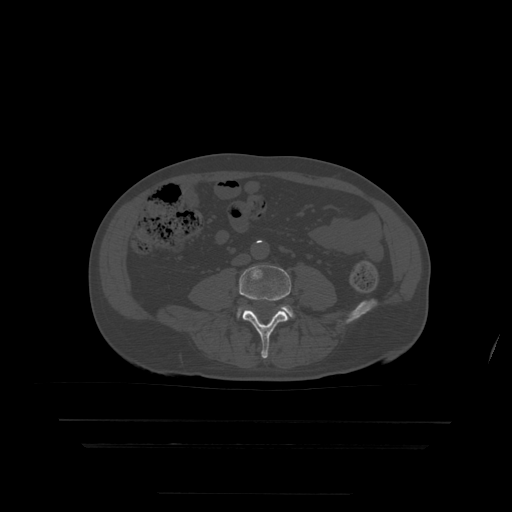
CT including the spine, one axial slice; position 91 of 522 along the scan axis; bone window (W 1800 / L 400 HU); 512 × 512 image matrix. Patient age 68 years. Case-level facts recorded for this patient, not image findings: primary cancer: urothelial.
Outlined on this slice (semi-automatic segmentation, software-assisted and operator-edited):
- L4 vertebra: bounding box (x1, y1, x2, y2) in pixels: (240, 266, 291, 359)
- L5 vertebra: (247, 306, 294, 317)